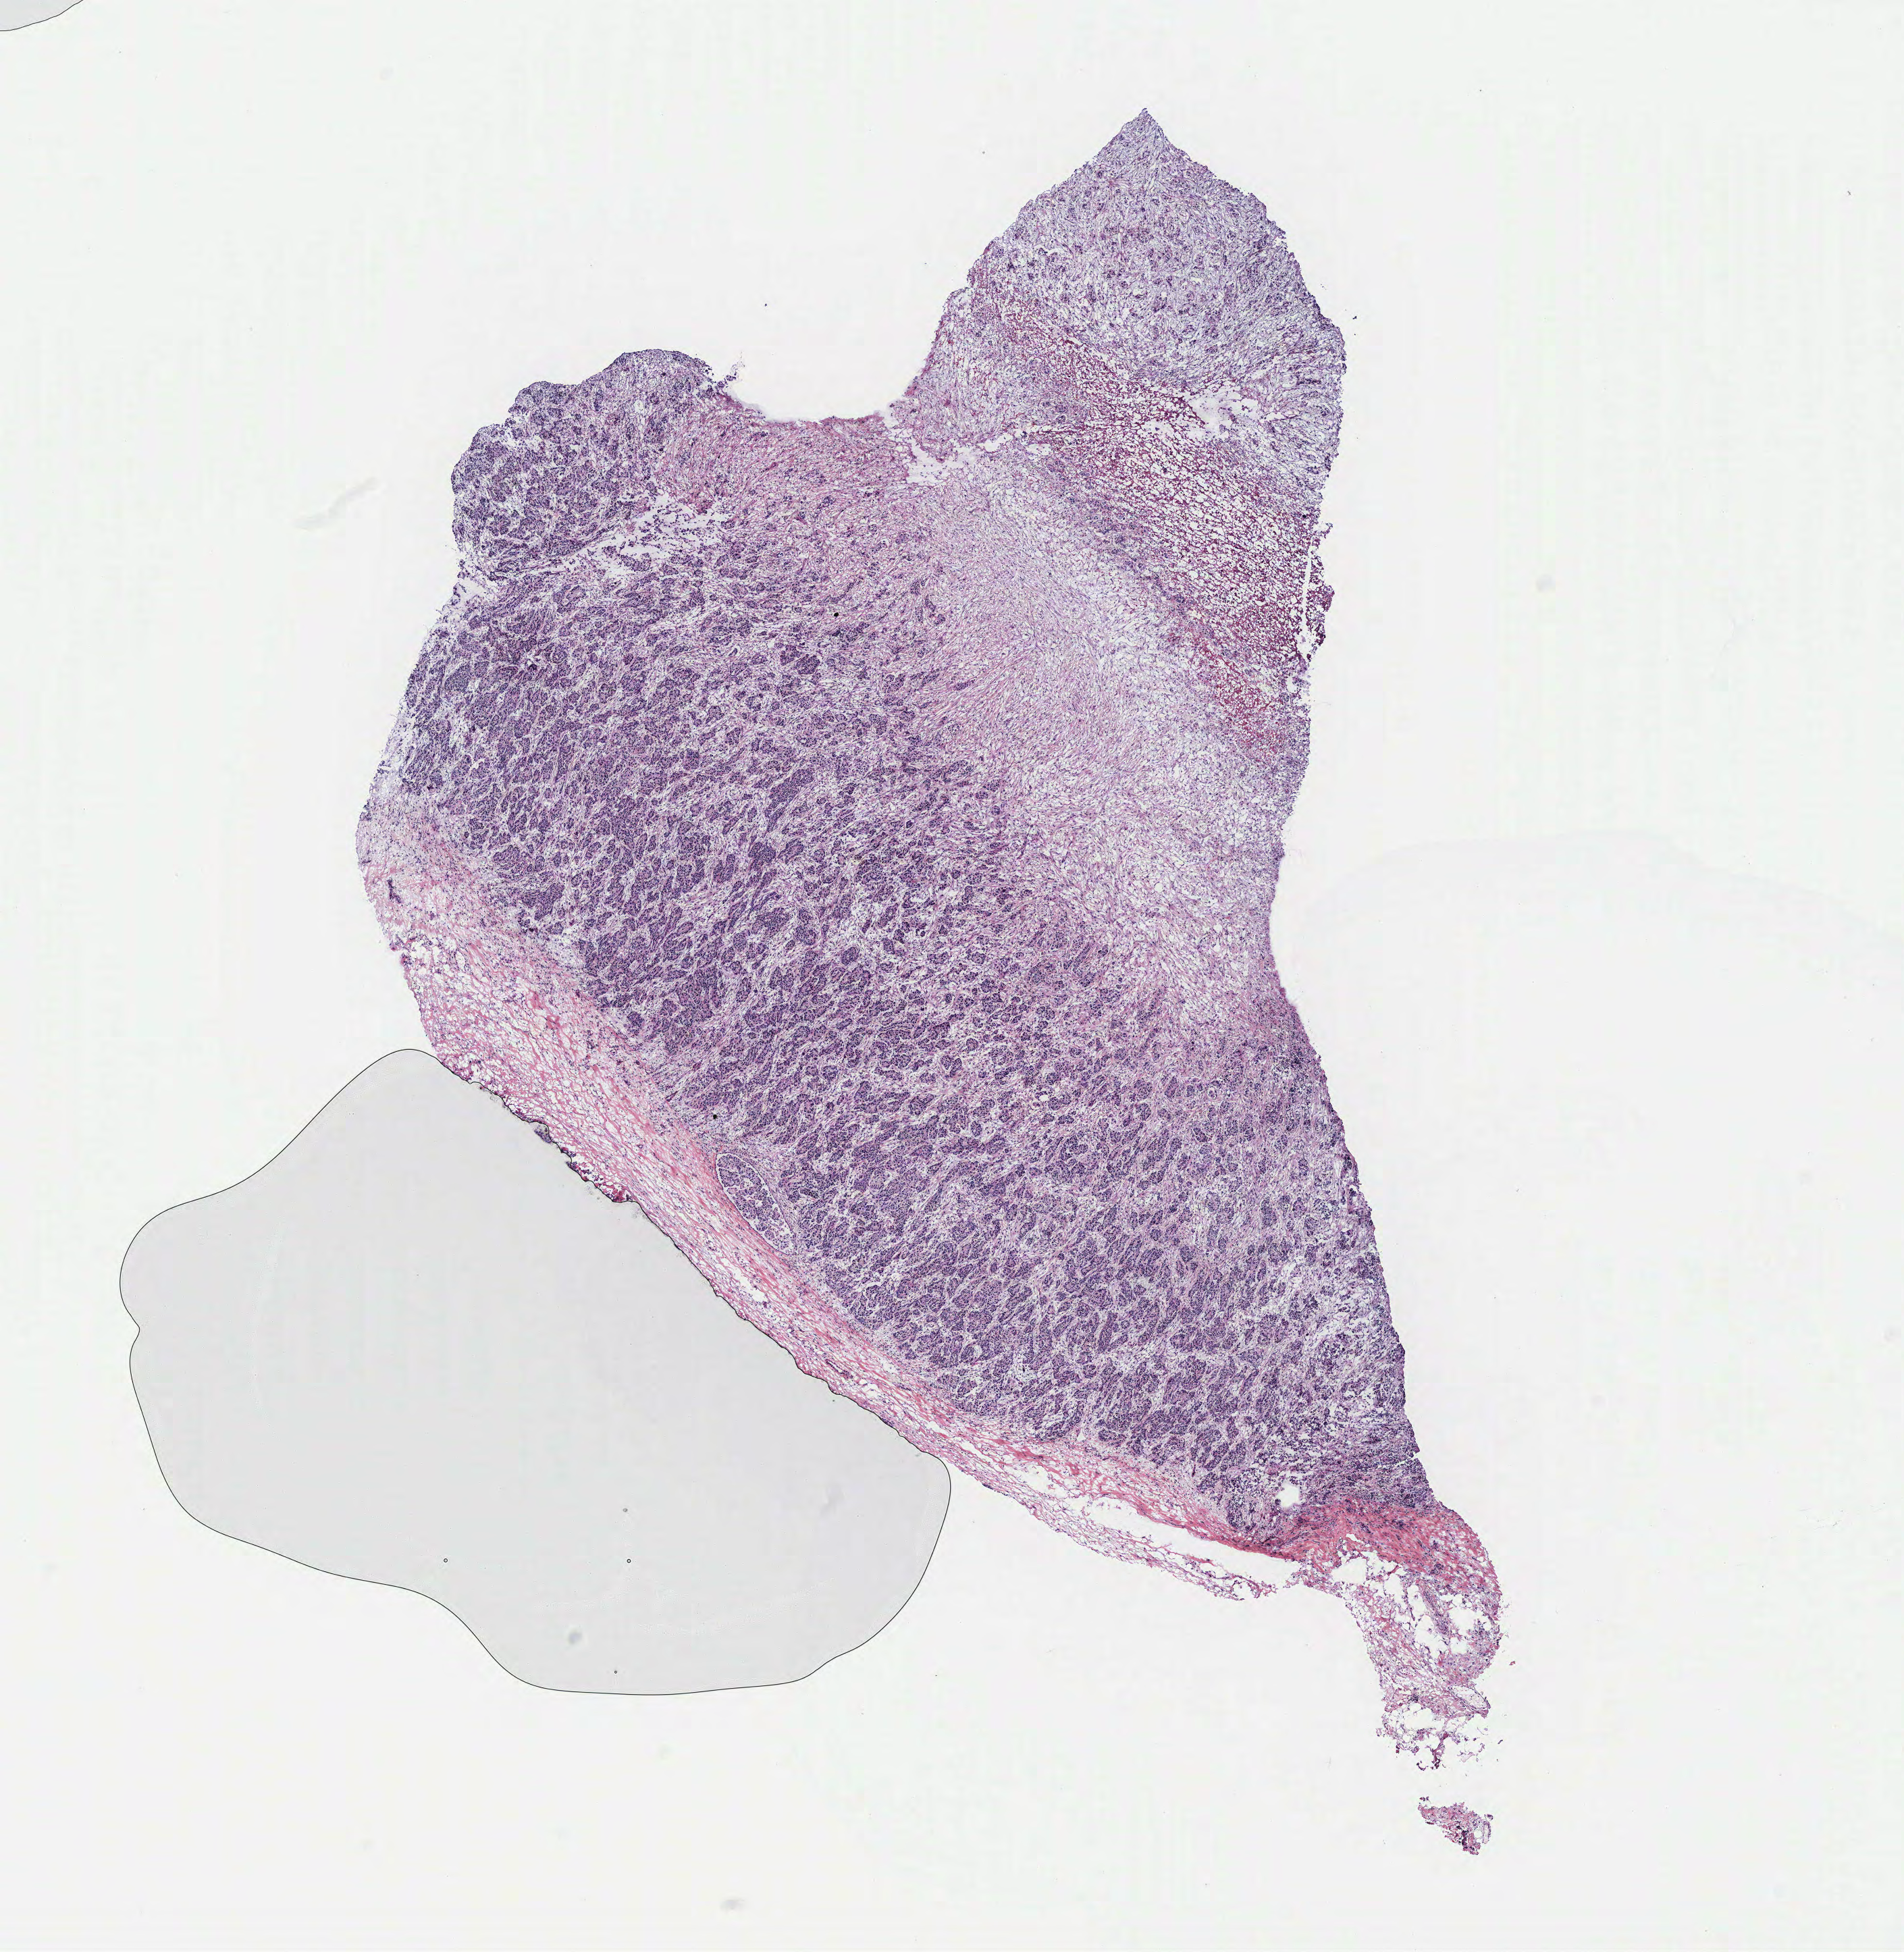
H&E-stained whole-slide image, whole scanned area (about 11.3 x 11.6 mm) shown as a low-resolution overview, ovary, tumour tissue. 69-year-old female patient.
Diagnosis: Serous adenocarcinoma, NOS.